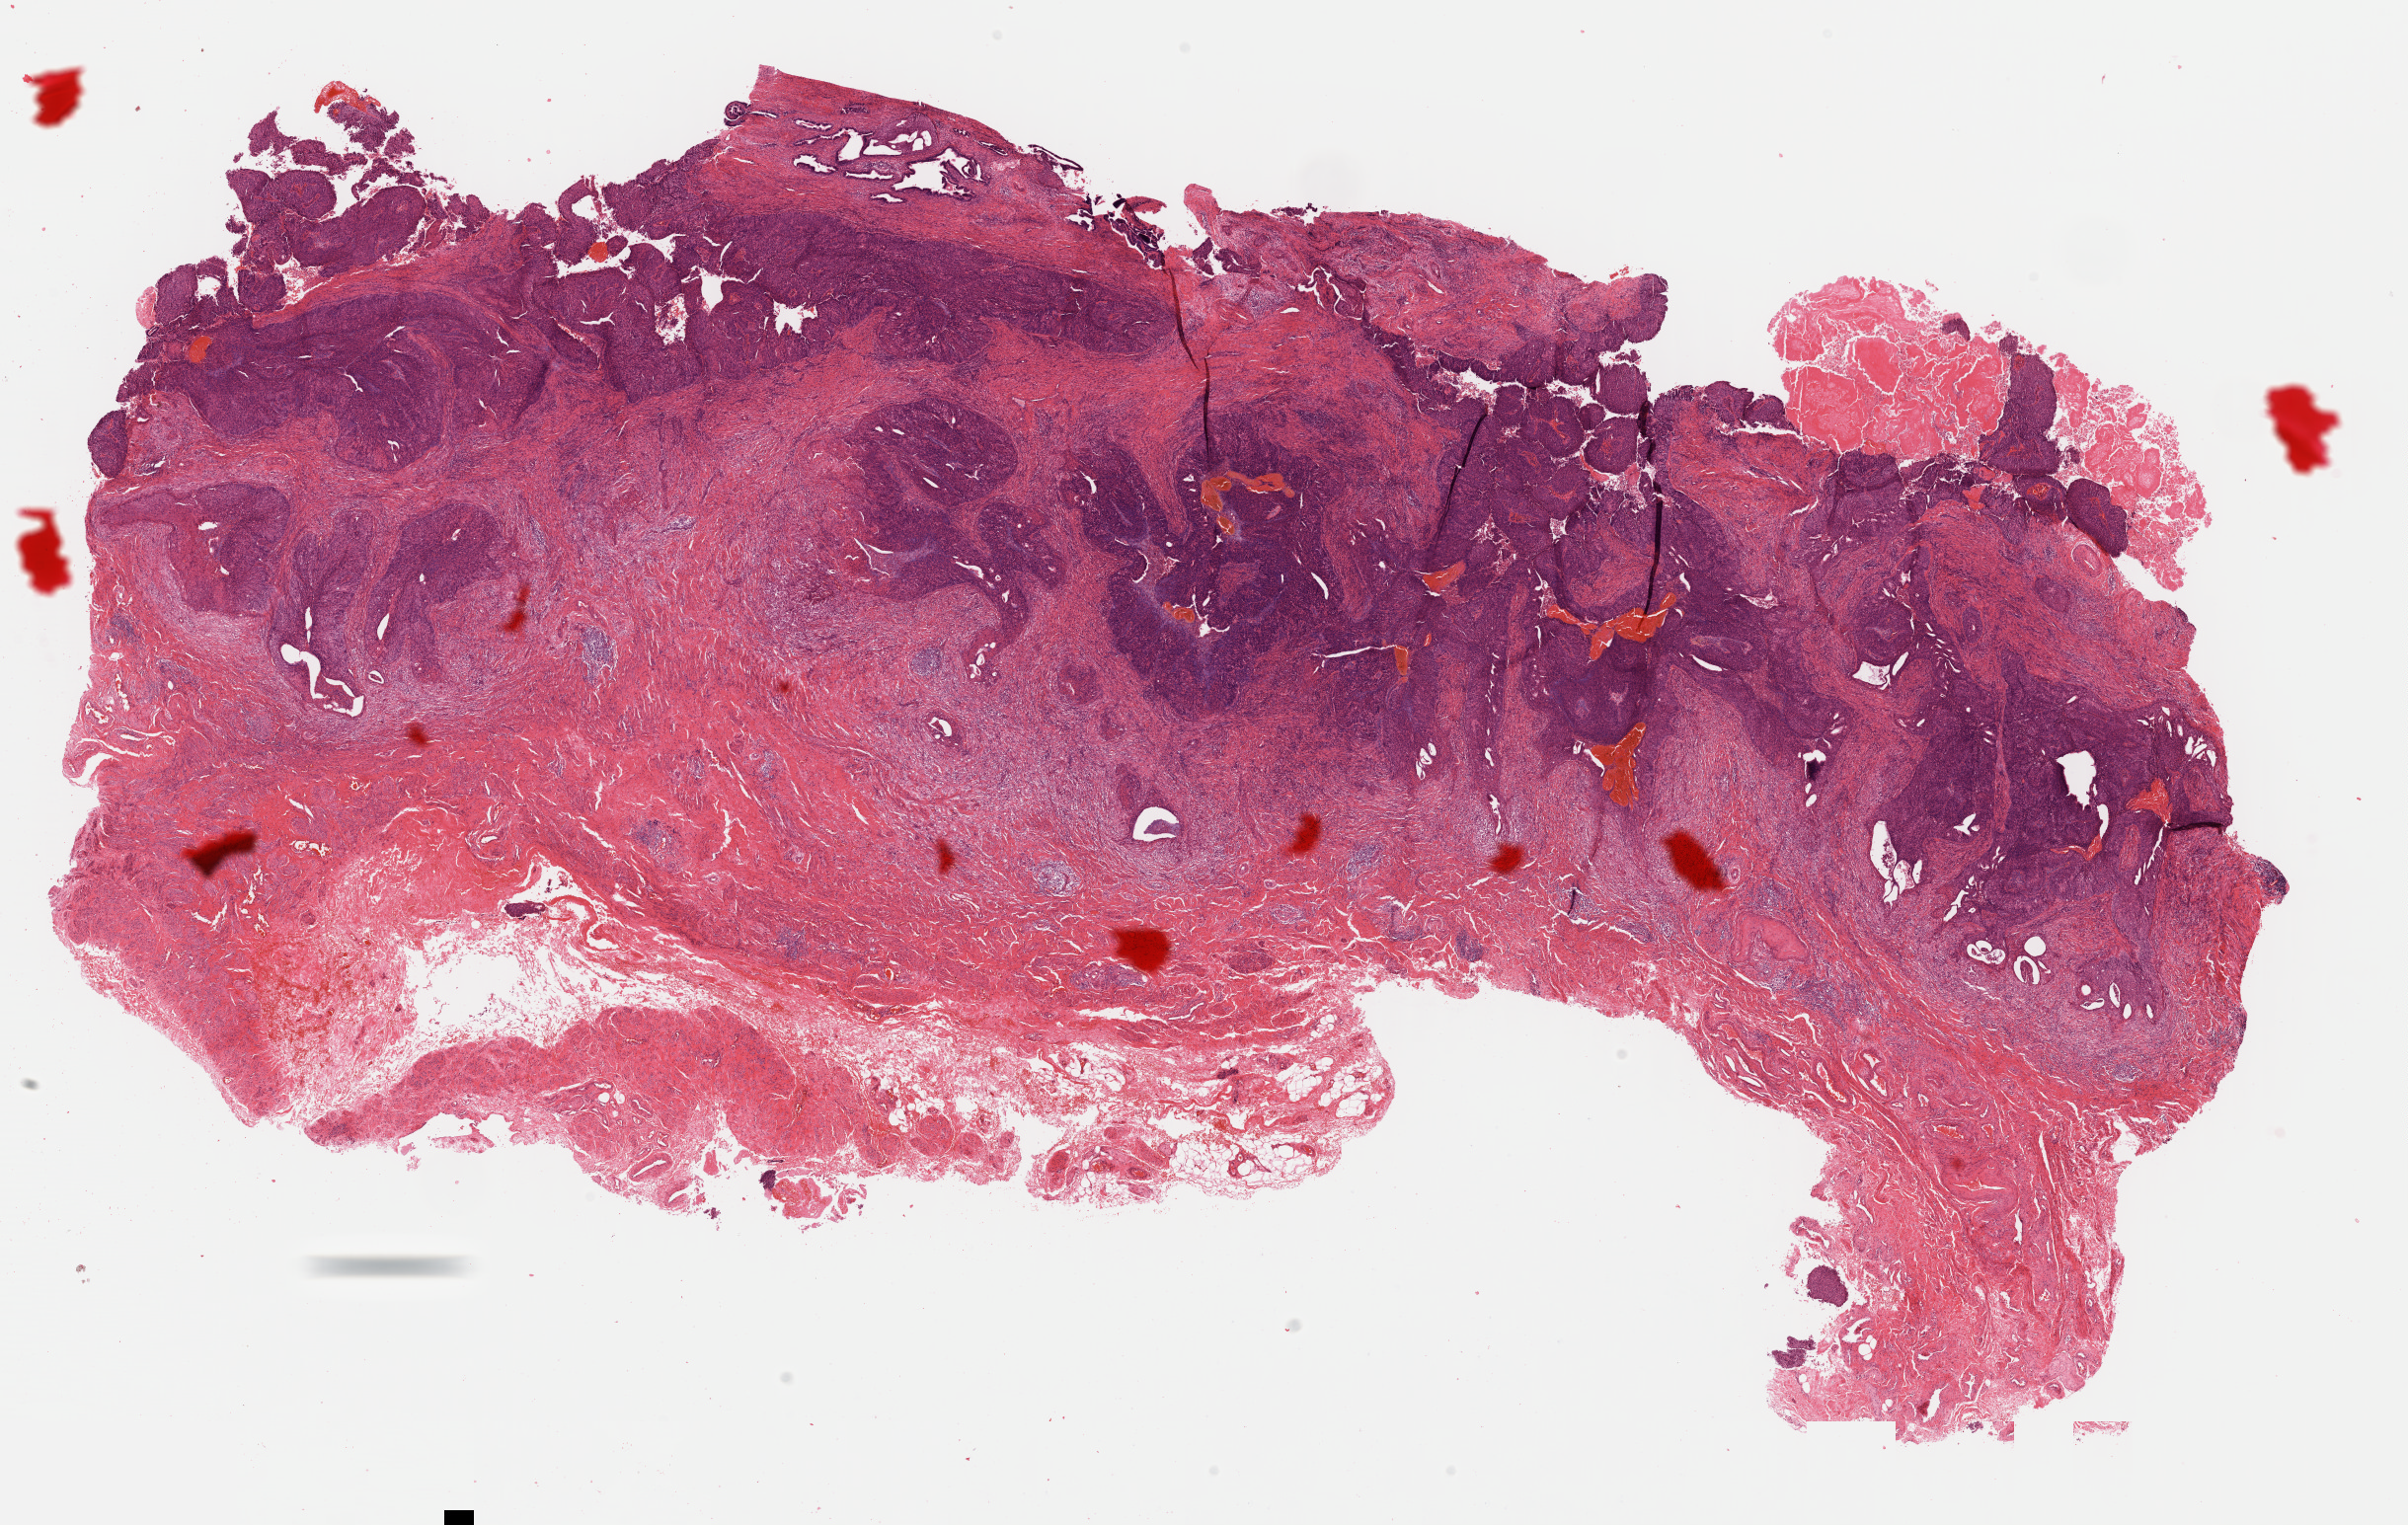
Digitized Hematoxylin and eosin (H&E) stained tissue section (whole slide), low-resolution overview of the scanned area, about 19.2 x 12.2 mm; formalin-fixed paraffin-embedded (FFPE) diagnostic section; sample: primary tumour, cervix. Patient: female, age at initial diagnosis 59 years. Histologic grade: G2 (moderately differentiated).
FIGO stage: IB1. Lymph nodes positive (case pathology): 0 of 21 examined. Histologic diagnosis: Squamous cell carcinoma, NOS (cervix uteri).